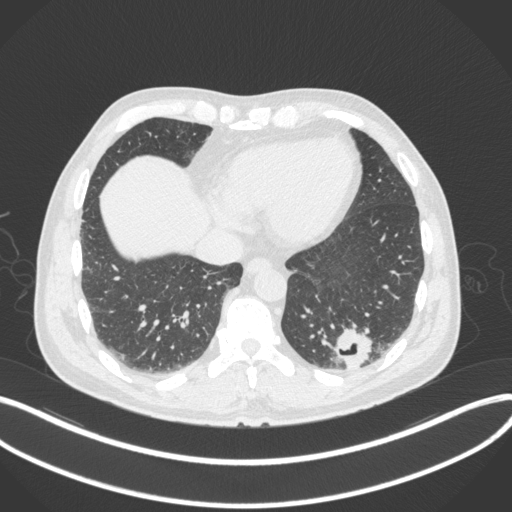
Chest CT, one axial slice. Position 75 of 313 along the scan axis. Reconstruction kernel B31f. Lung window (W 1500 / L -600 HU). 512 × 512 image matrix, field of view 400 × 400 mm. Patient: male, 54 years. Case-level facts recorded for this patient, not image findings: clinical TNM (as recorded): T1c N0 M1.
Structures marked on this image (rectangle marked by the reading radiologist):
- lung tumour (recorded histology: adenocarcinoma): bounding box (x1, y1, x2, y2) in pixels: (333, 322, 373, 369)